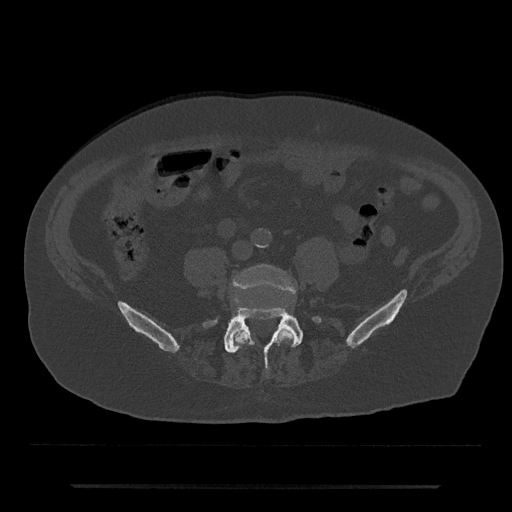
CT including the spine, one axial slice; slice 312 of 797 in the series (ordered by position); reconstruction kernel Br40s/3; 120 kVp; bone window (W 1800 / L 400 HU); 512 × 512 image matrix, field of view 434 × 434 mm. Male patient, age 80 years. From the clinical record (not read from this slice): primary cancer: prostate.
Annotated regions visible in this slice (semi-automatic segmentation, software-assisted and operator-edited):
- L4 vertebra: box from (x=232, y=264) to (x=296, y=347) px
- L5 vertebra: (x=204, y=307)–(x=321, y=369)